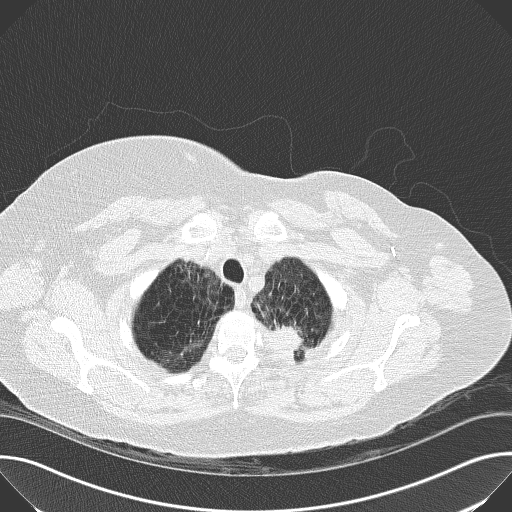
Low-dose screening chest CT, one axial slice. Reconstruction kernel B50f. Lung window (W 1500 / L -600 HU). 2 mm slice thickness. 512 × 512 image matrix.
Outlined on this slice (expert manual segmentation):
- lesion 1 (tumor, upper lobe of left lung): bounding box <273,323,311,359> (left, top, right, bottom; pixels)